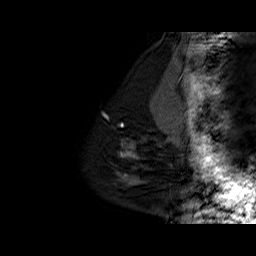
Breast MRI (dynamic contrast-enhanced), one sagittal slice; slice 10 of 60 in the series (ordered by position); dynamic contrast-enhanced series, time point 2 of 6 at this slice position (early post-contrast); 1.5 T; TE 6.3 ms, TR 32.5 ms; 4 mm slice thickness; 256 × 256 image matrix, field of view 200 × 200 mm. Female patient. Case-level facts recorded for this patient, not image findings: setting: breast cancer imaged before/during neoadjuvant chemotherapy; receptor status: triple-negative.
Structures marked on this image (semi-automatic segmentation, software-assisted and operator-edited):
- analysis volume of interest (the breast-tissue region the enhancement analysis was run in; not a lesion): bounding box (x1, y1, x2, y2) in pixels: (111, 127, 162, 186)
- tumour enhancement mask (voxels above the 100 % enhancement threshold inside the analysis volume of interest): (120, 146, 133, 157)